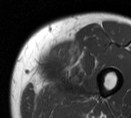
MRI of an extremity soft-tissue mass, one axial slice; slice 16 of 55 in the series (ordered by position); MR volume resampled by the dataset authors to the PET/CT grid (not the native acquisition matrix); 3.27 mm slice thickness; 131 × 118 image matrix, field of view 128 × 115 mm. Male patient. From the clinical record (not read from this slice): histological type: pleiomorphic liposarcoma; grade: high; site of the primary tumour: left thigh.
Annotated regions visible in this slice (expert contour drawn on MRI and transferred to this co-registered scan by the dataset authors):
- gross tumour volume including surrounding oedema: bounding box [x1, y1, x2, y2] px = [30, 43, 94, 101]
- gross tumour volume (mass): [30, 41, 69, 90]